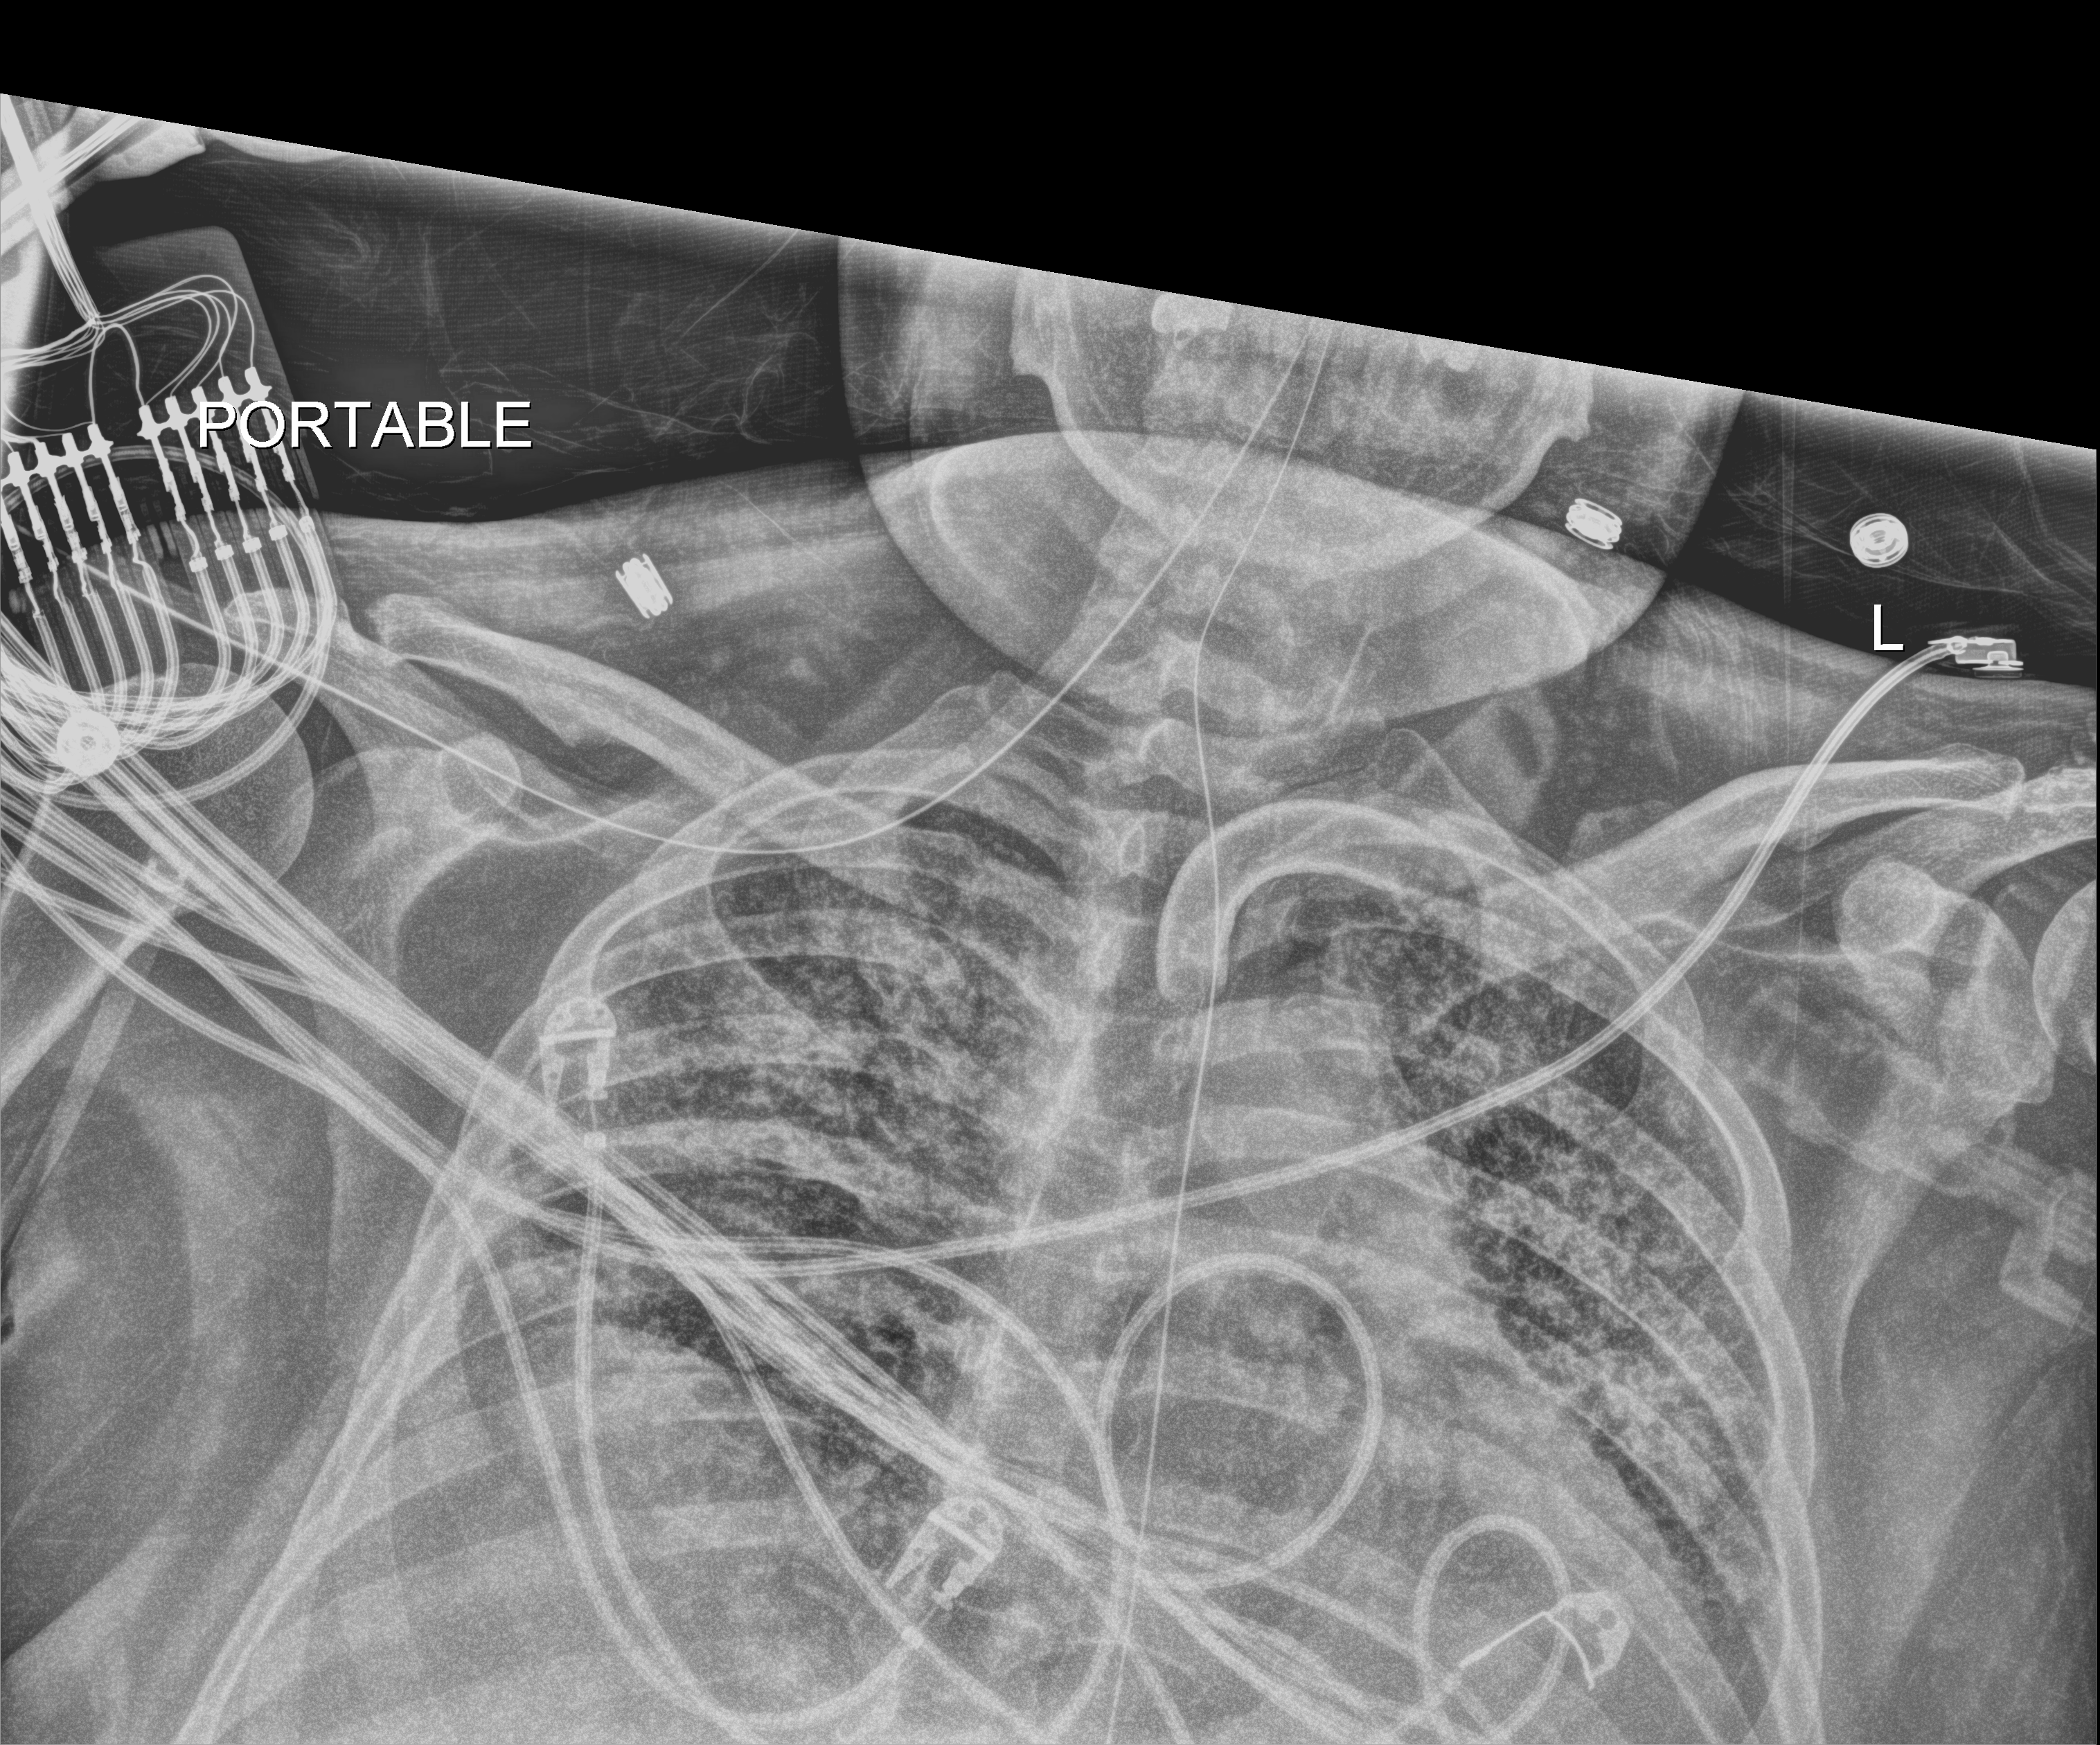
Bedside chest radiograph (digital radiography); anteroposterior (AP) projection. Male patient hospitalised with COVID-19, age 18–59 years.
Hospital-stay facts (about this admission, not read from this image; timing relative to this image not recorded): chronic kidney disease (admission record): no.